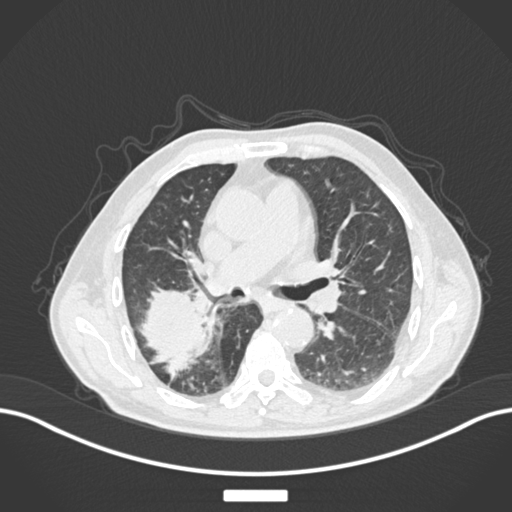
Chest CT, one axial slice; slice 97 of 201 in the series (ordered by position); reconstruction kernel B30f; lung window (W 1500 / L -600 HU); 1 mm slice thickness; 512 × 512 image matrix, field of view 400 × 400 mm. Male patient, age 72 years. Case-level facts recorded for this patient, not image findings: clinical TNM (as recorded): T3 N2 M0.
Outlined on this slice (bounding box drawn by a radiologist):
- lung tumour (recorded histology: adenocarcinoma): bounding box (x1, y1, x2, y2) in pixels: (135, 283, 210, 379)